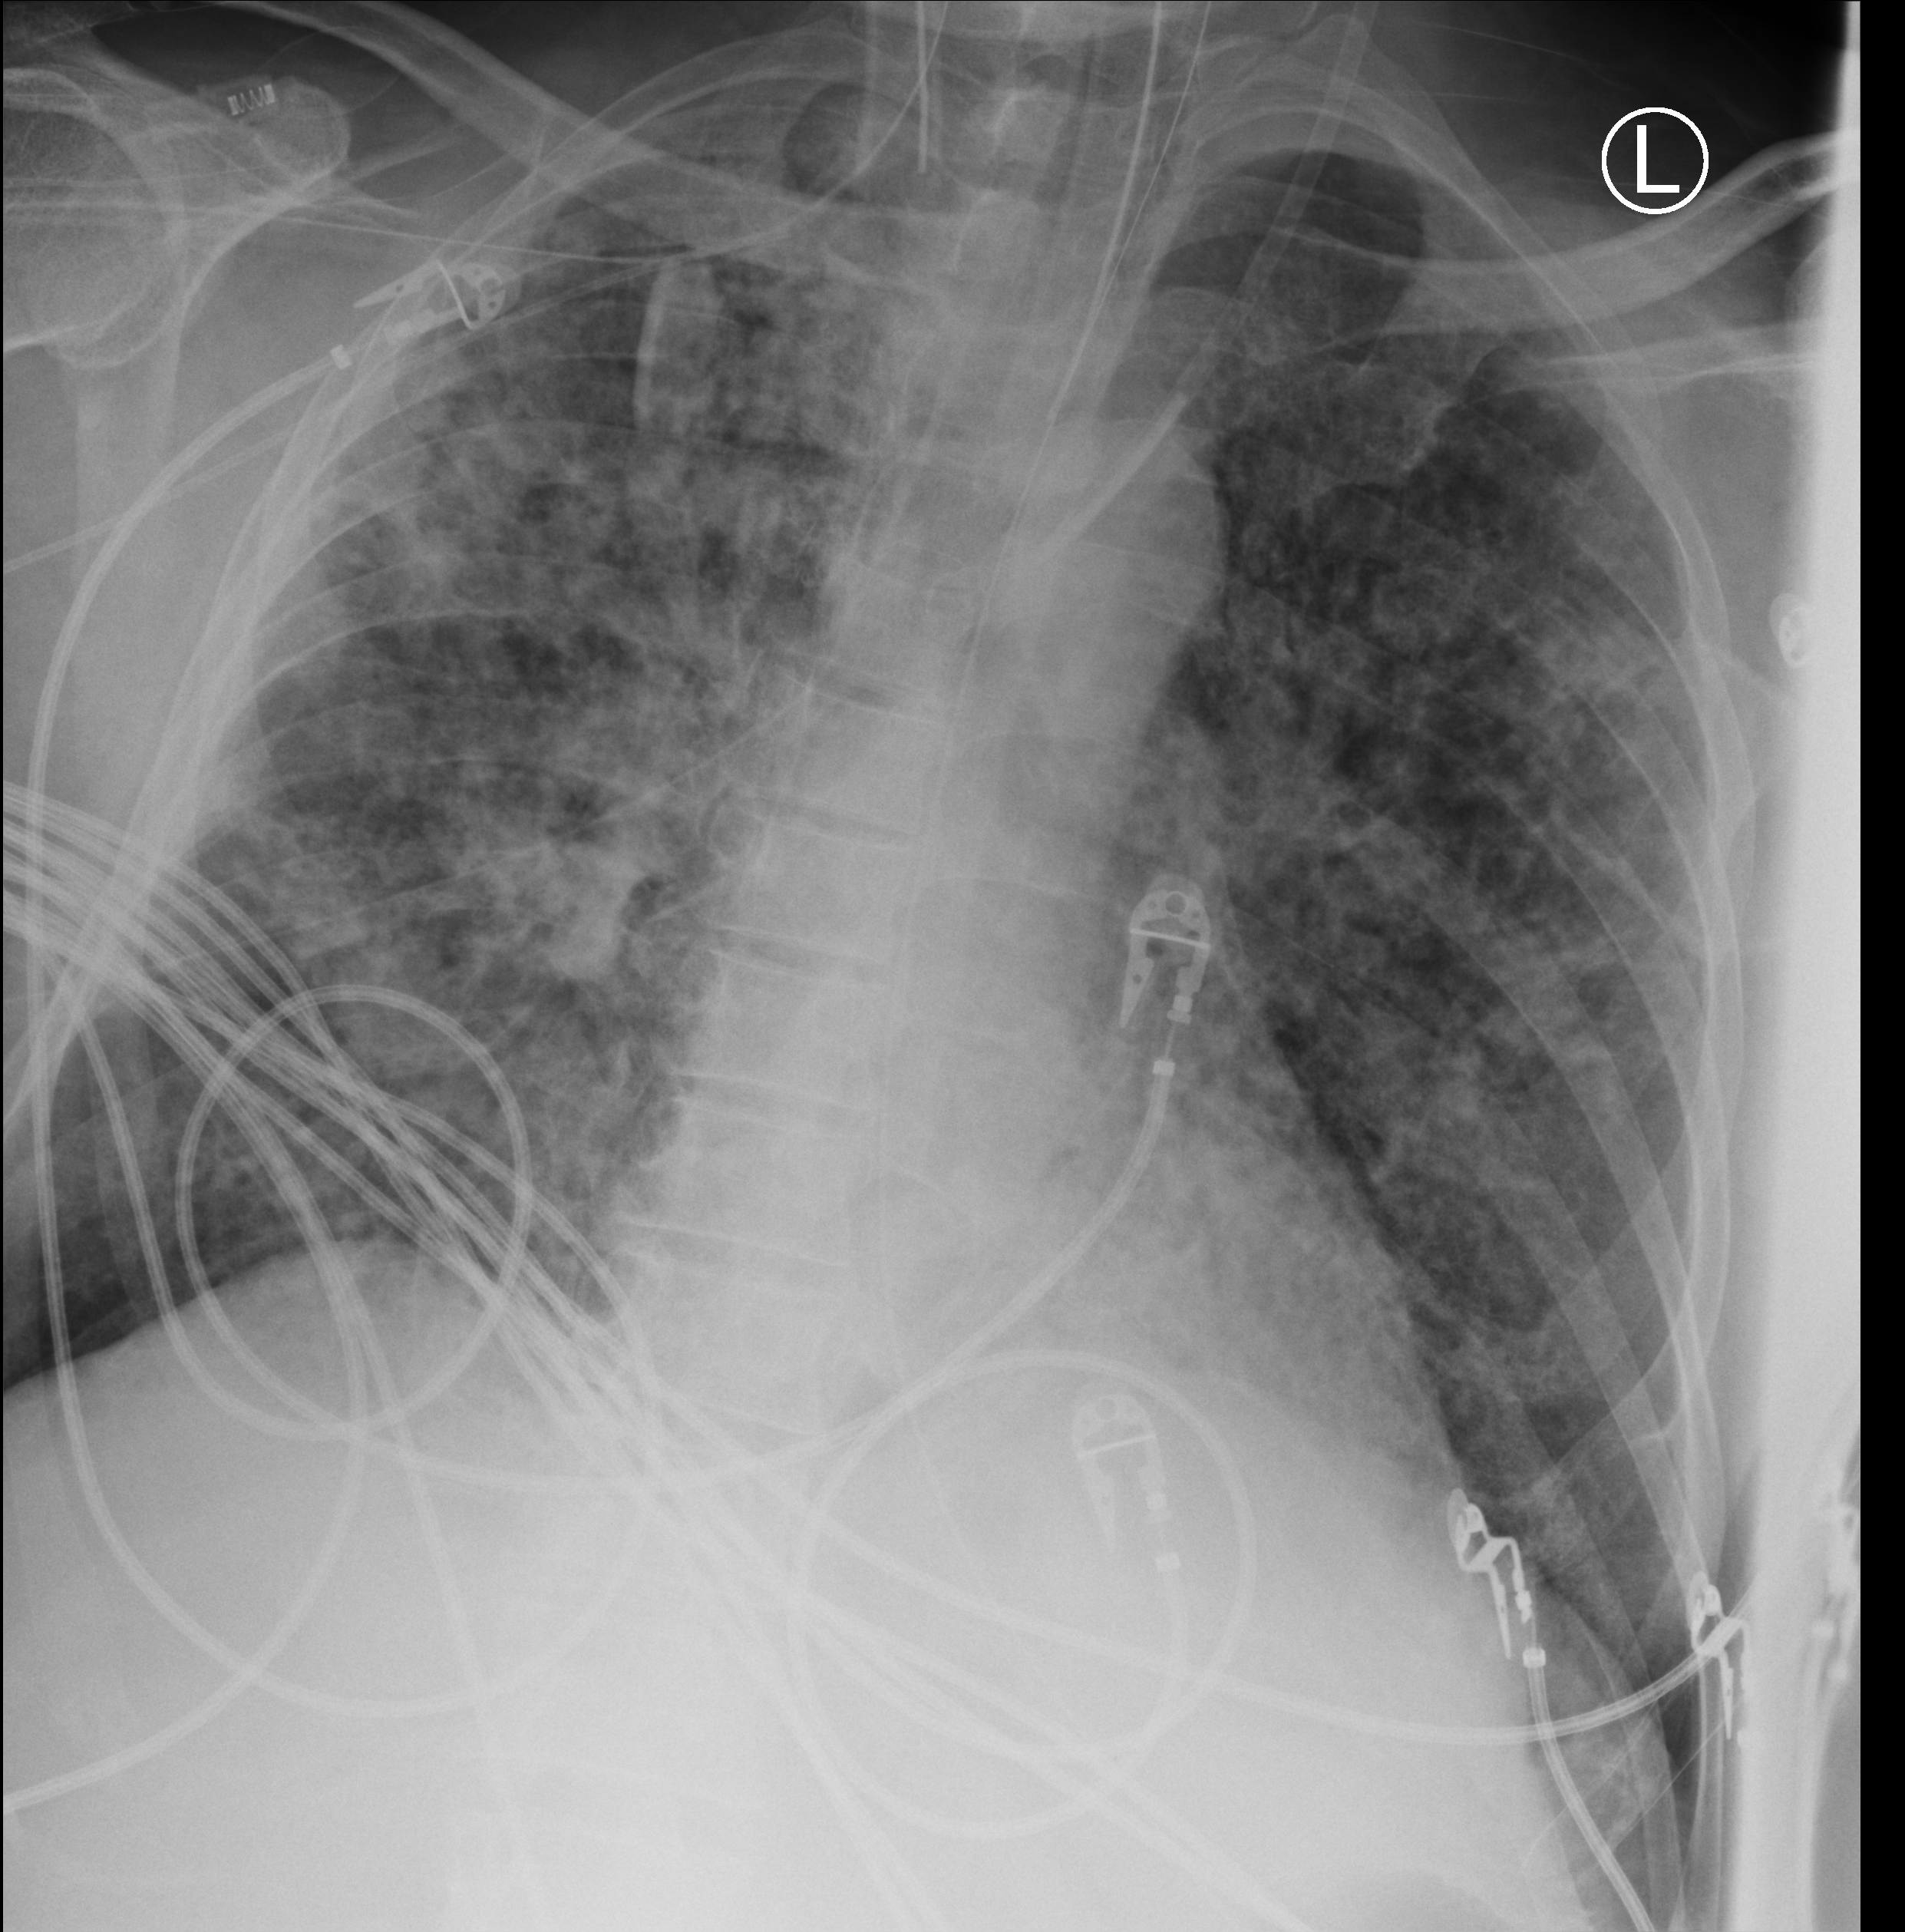
Bedside chest radiograph (computed radiography), anteroposterior (AP) projection. Male patient hospitalised with COVID-19, age 60–74 years.
Admission-level facts for this patient (not findings on this image; timing relative to this image not recorded): mechanically ventilated during this hospital stay: yes; length of hospital stay: 6 days; admitted to intensive care during this hospital stay: yes.